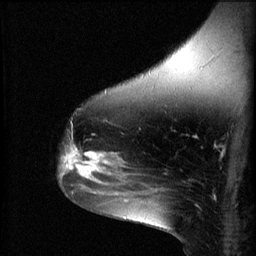
Breast MRI (dynamic contrast-enhanced), one sagittal slice. Position 43 of 60 along the scan axis. 3 images stored at this slice position (order not interpretable as contrast timing). 1.5 T. TE 4.2 ms, TR 8.2 ms. 256 × 256 image matrix. Patient: female, 49 years.
Outlined on this slice (semi-automatic segmentation, software-assisted and operator-edited):
- analysis volume of interest (the breast-tissue region the enhancement analysis was run in; not a lesion): box from (x=59, y=142) to (x=109, y=187) px
- tumour enhancement mask (voxels above the 70 % enhancement threshold inside the analysis volume of interest): (x=60, y=144)–(x=109, y=185)